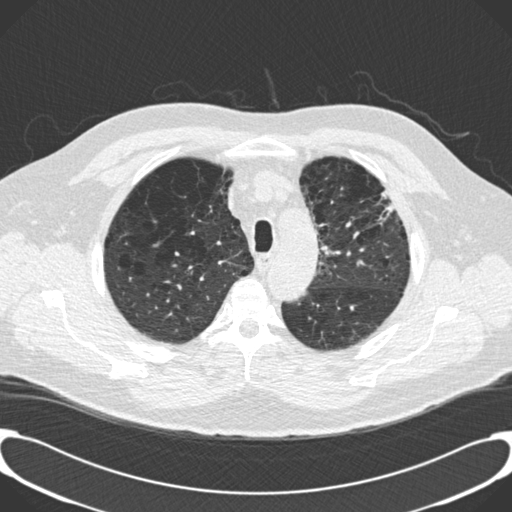
Low-dose screening chest CT, one axial slice. Slice 157 of 189 in the series (ordered by position). Reconstruction kernel B30f. 120 kVp. Lung window (W 1500 / L -600 HU). 2 mm slice thickness. 512 × 512 image matrix, field of view 380 × 380 mm.
Annotated regions visible in this slice (expert manual segmentation):
- lesion 1 (tumor, upper lobe of left lung): bounding box <379,190,394,224> (left, top, right, bottom; pixels)